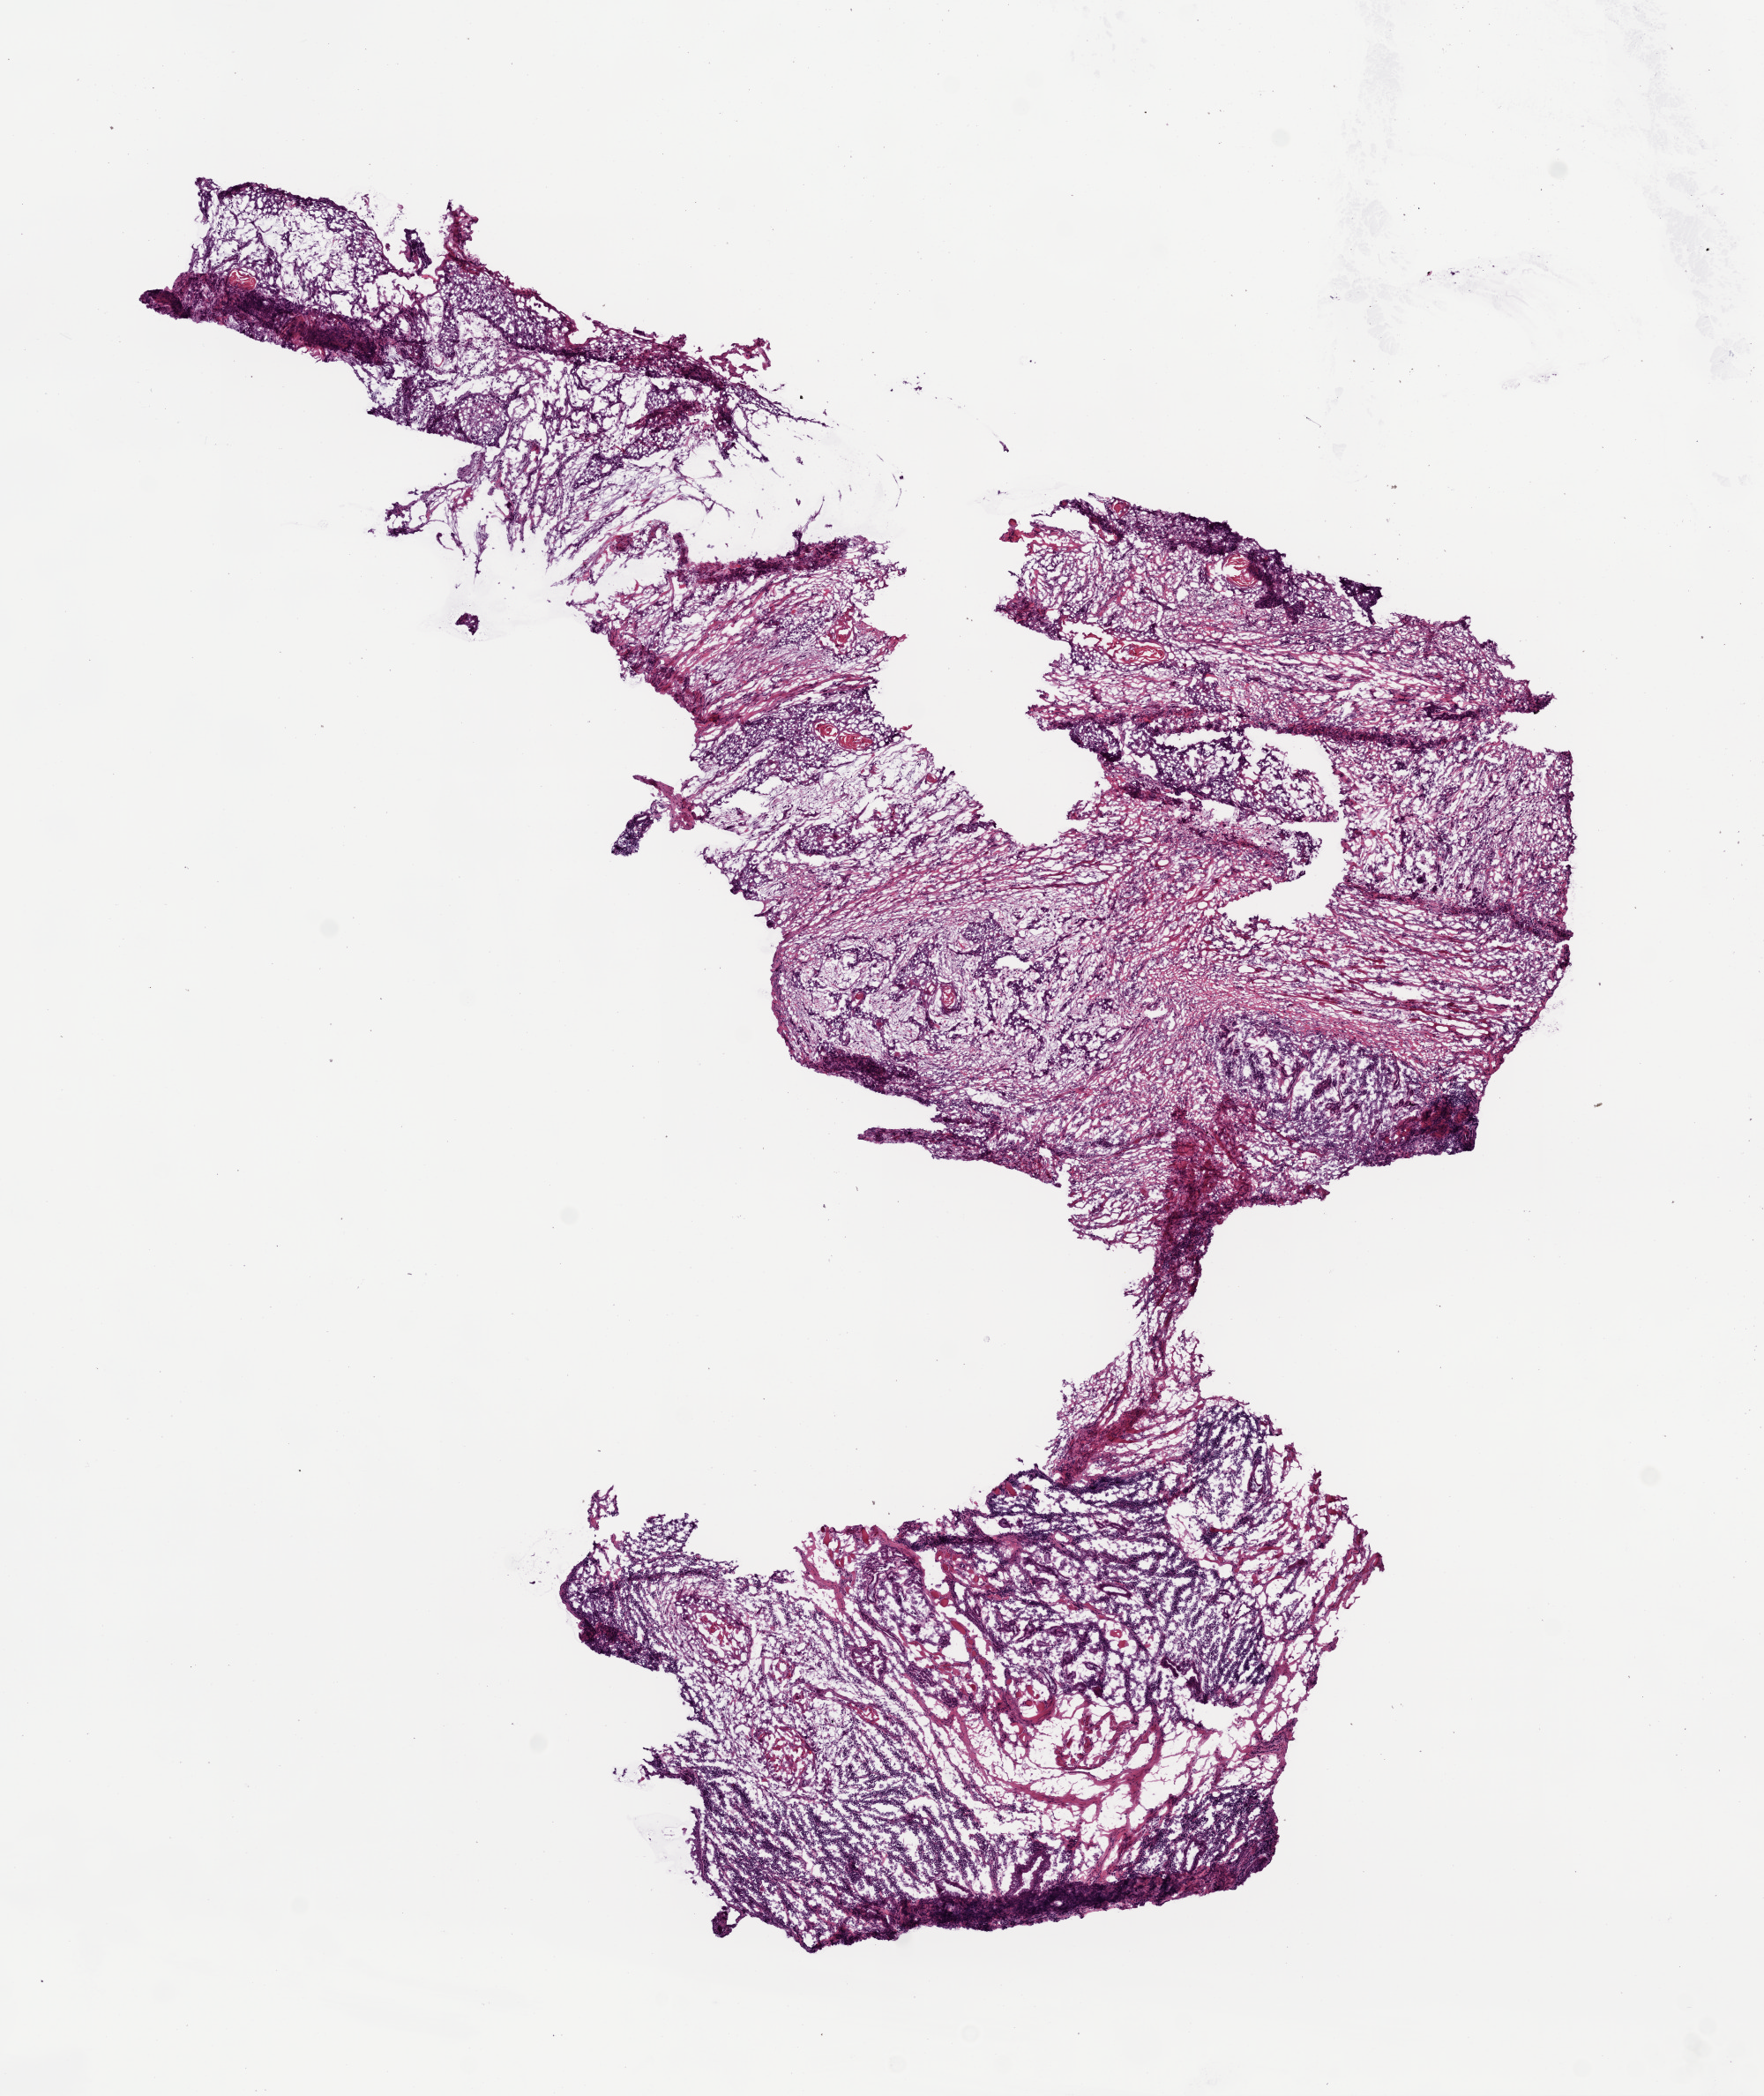
Digitized H&E tissue section (whole slide) — a low-resolution overview of the entire scanned area, about 8.0 x 9.5 mm, frozen section, primary tumour sample from the head and neck. Male, age 68 years at initial diagnosis. Histologic grade: G3 (poorly differentiated). Slide review estimates, as recorded: tumour cells 30%, tumour nuclei 30%, normal cells 0%, stromal cells 70%, necrosis 0%.
AJCC pathologic stage: III (7th edition). Diagnosis: Squamous cell carcinoma, NOS (larynx, NOS). TNM: T3 N0.